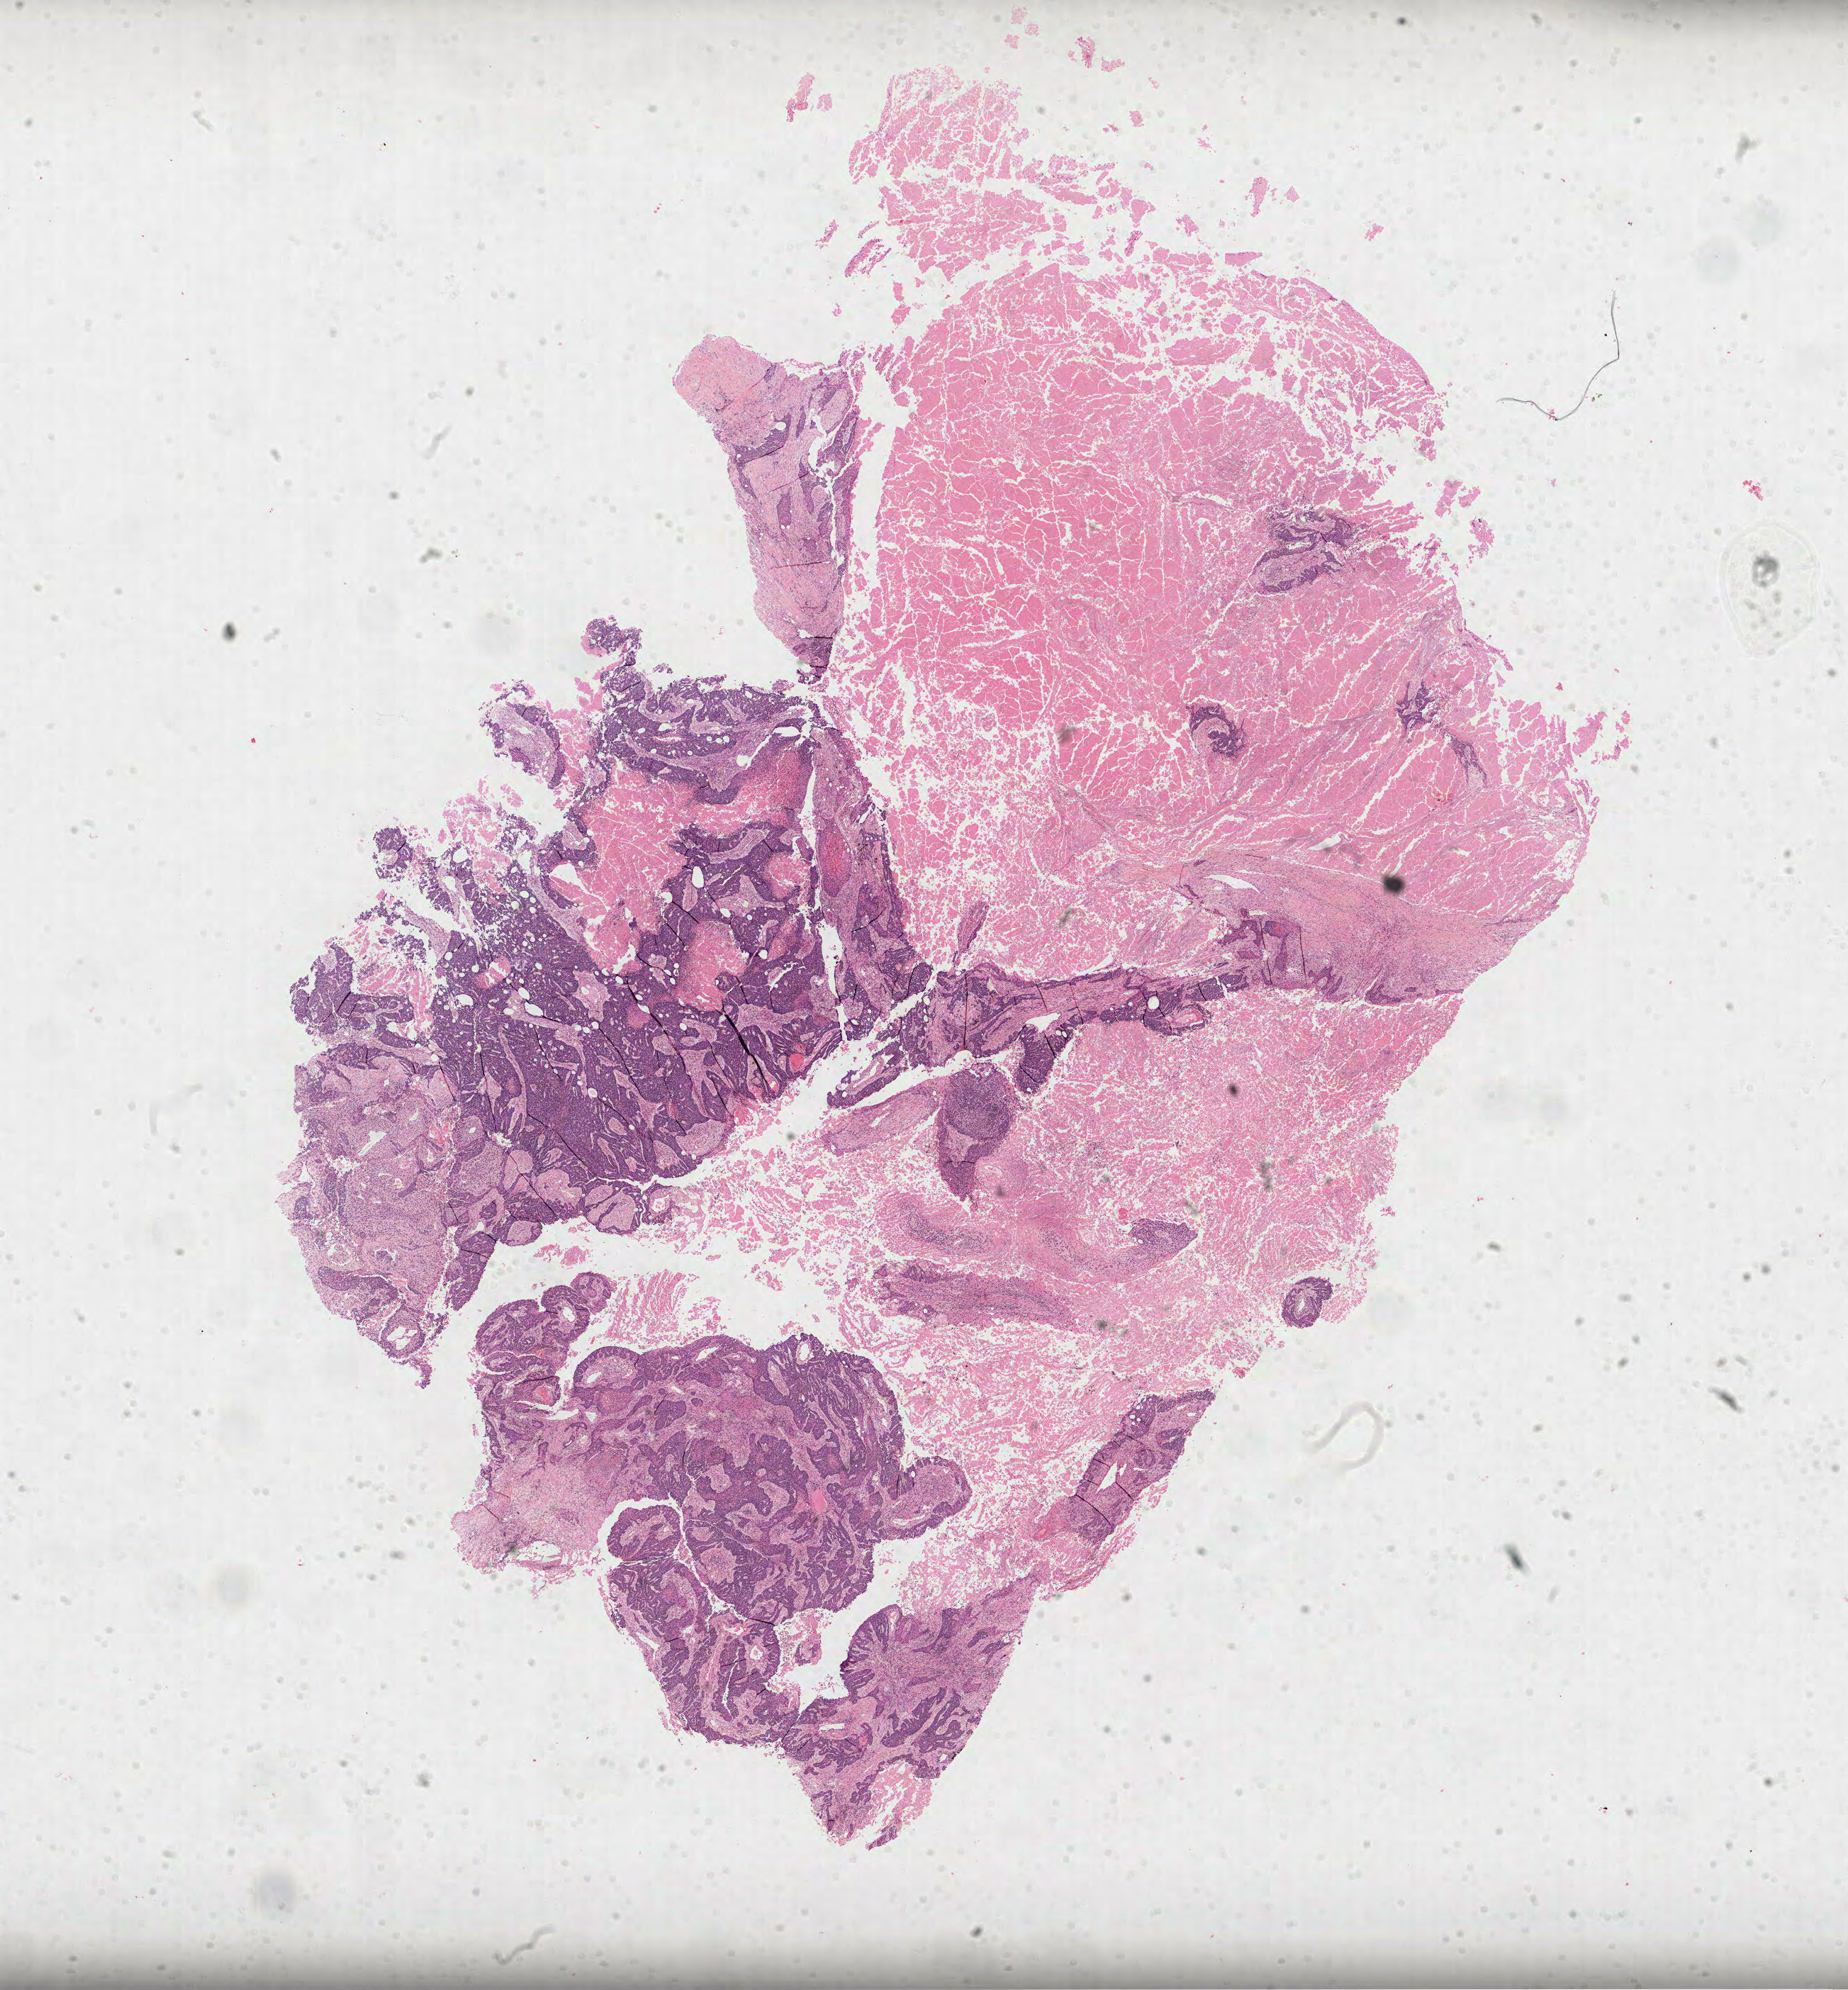
Digitized Hematoxylin and eosin (H&E) stained tissue section (whole slide) — whole scanned area (about 21.0 x 22.6 mm) shown as a low-resolution overview, formalin-fixed paraffin-embedded (FFPE) diagnostic section, sample: primary tumour, lung. Male patient; age at initial diagnosis 76 years.
Histologic diagnosis: Squamous cell carcinoma, NOS (upper lobe, lung).